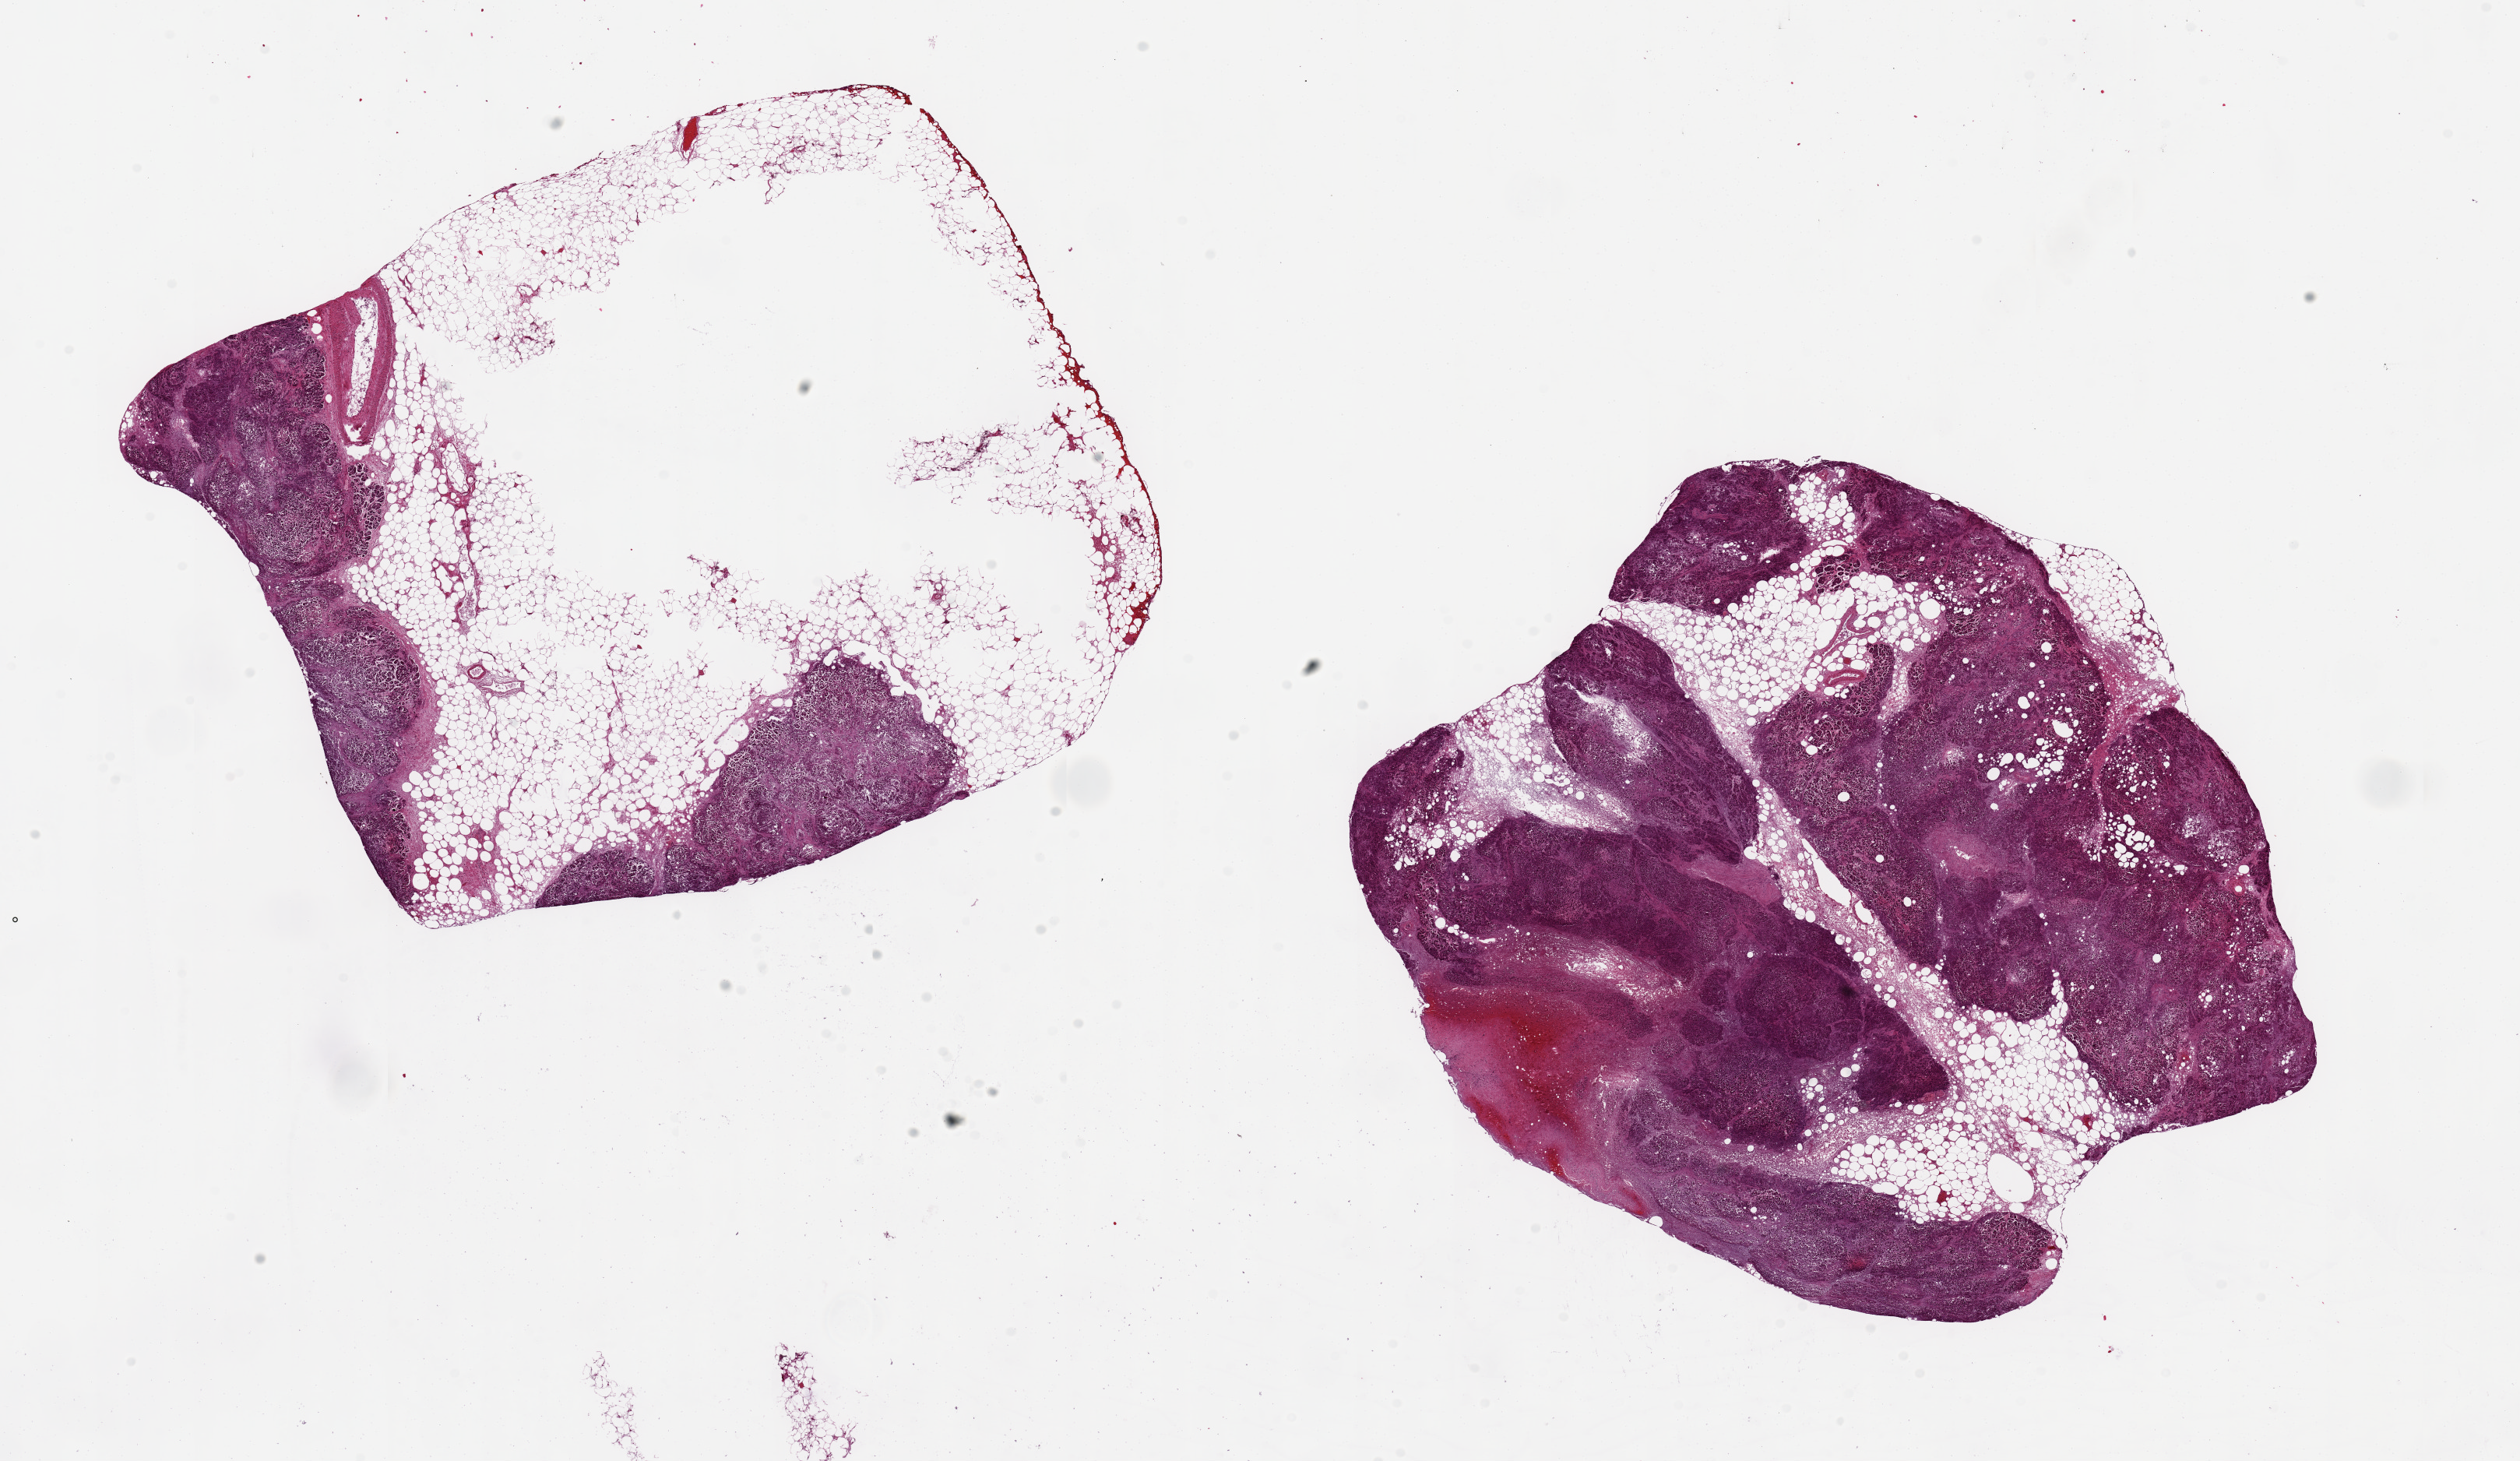
Digitized H&E-stained section, brightfield, shown as a low-resolution overview of the whole scanned area (about 25.6 x 14.8 mm).
Specimen: PAXgene-fixed, paraffin-embedded tissue; sampled site (target tissue): pancreas; tissue donor sample.